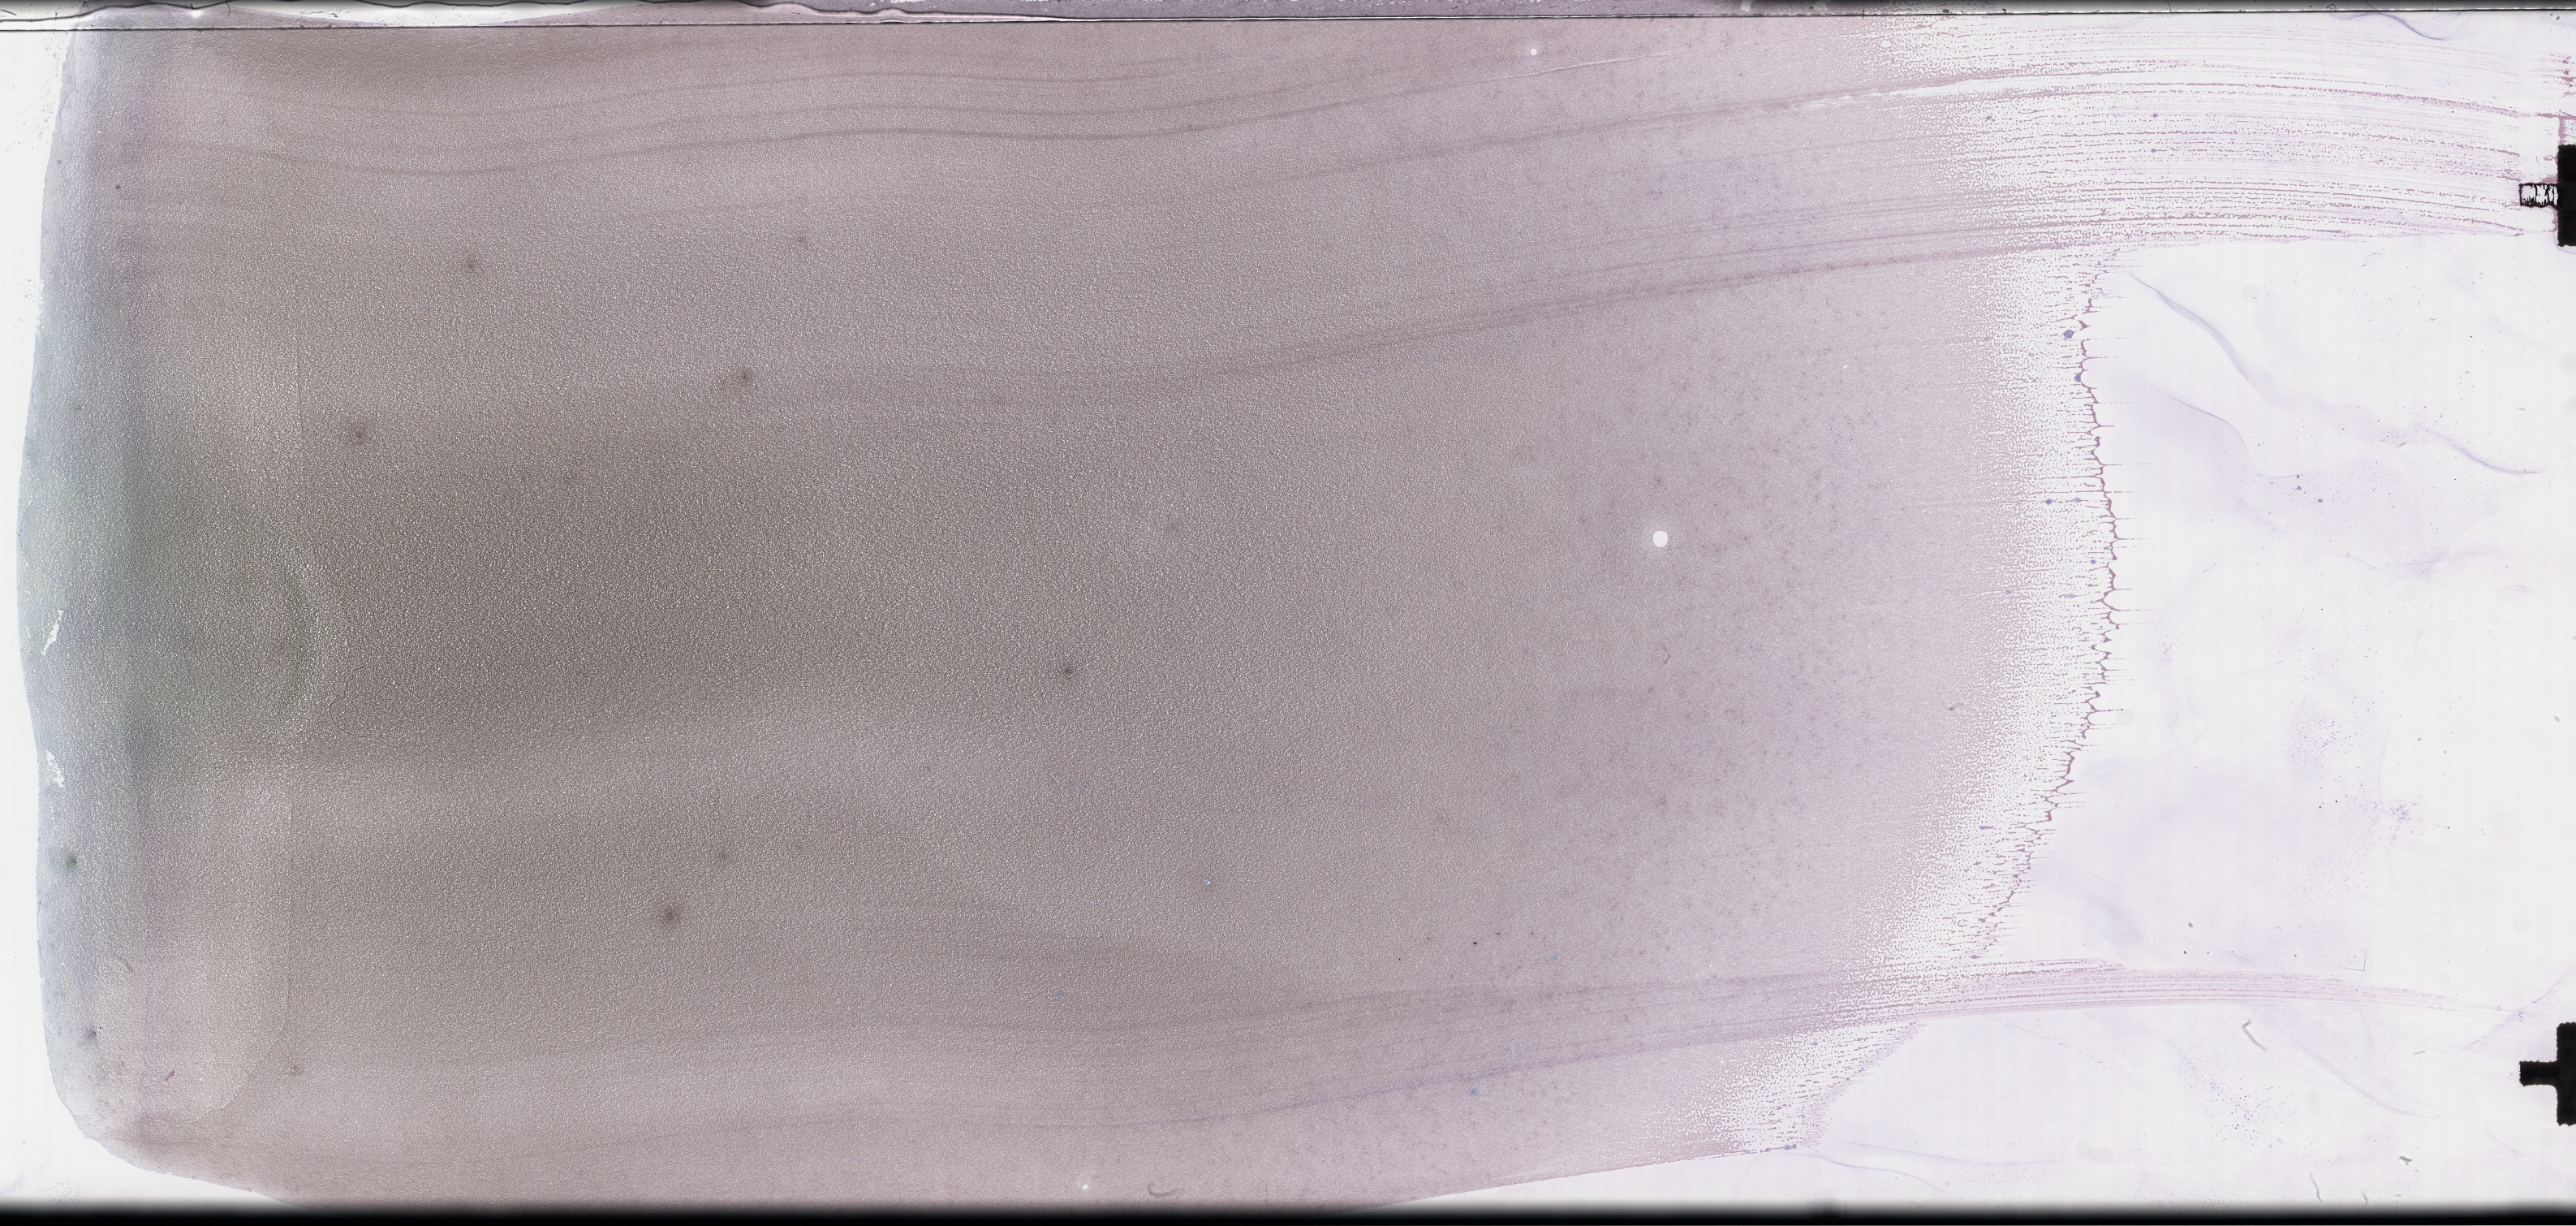
Whole-slide image of a whole blood smear, Wright–Giemsa stain, whole scanned area (about 51.3 x 24.4 mm) shown as a low-resolution overview. Patient sex: male.
From a patient with: Plasma Cell Myeloma.